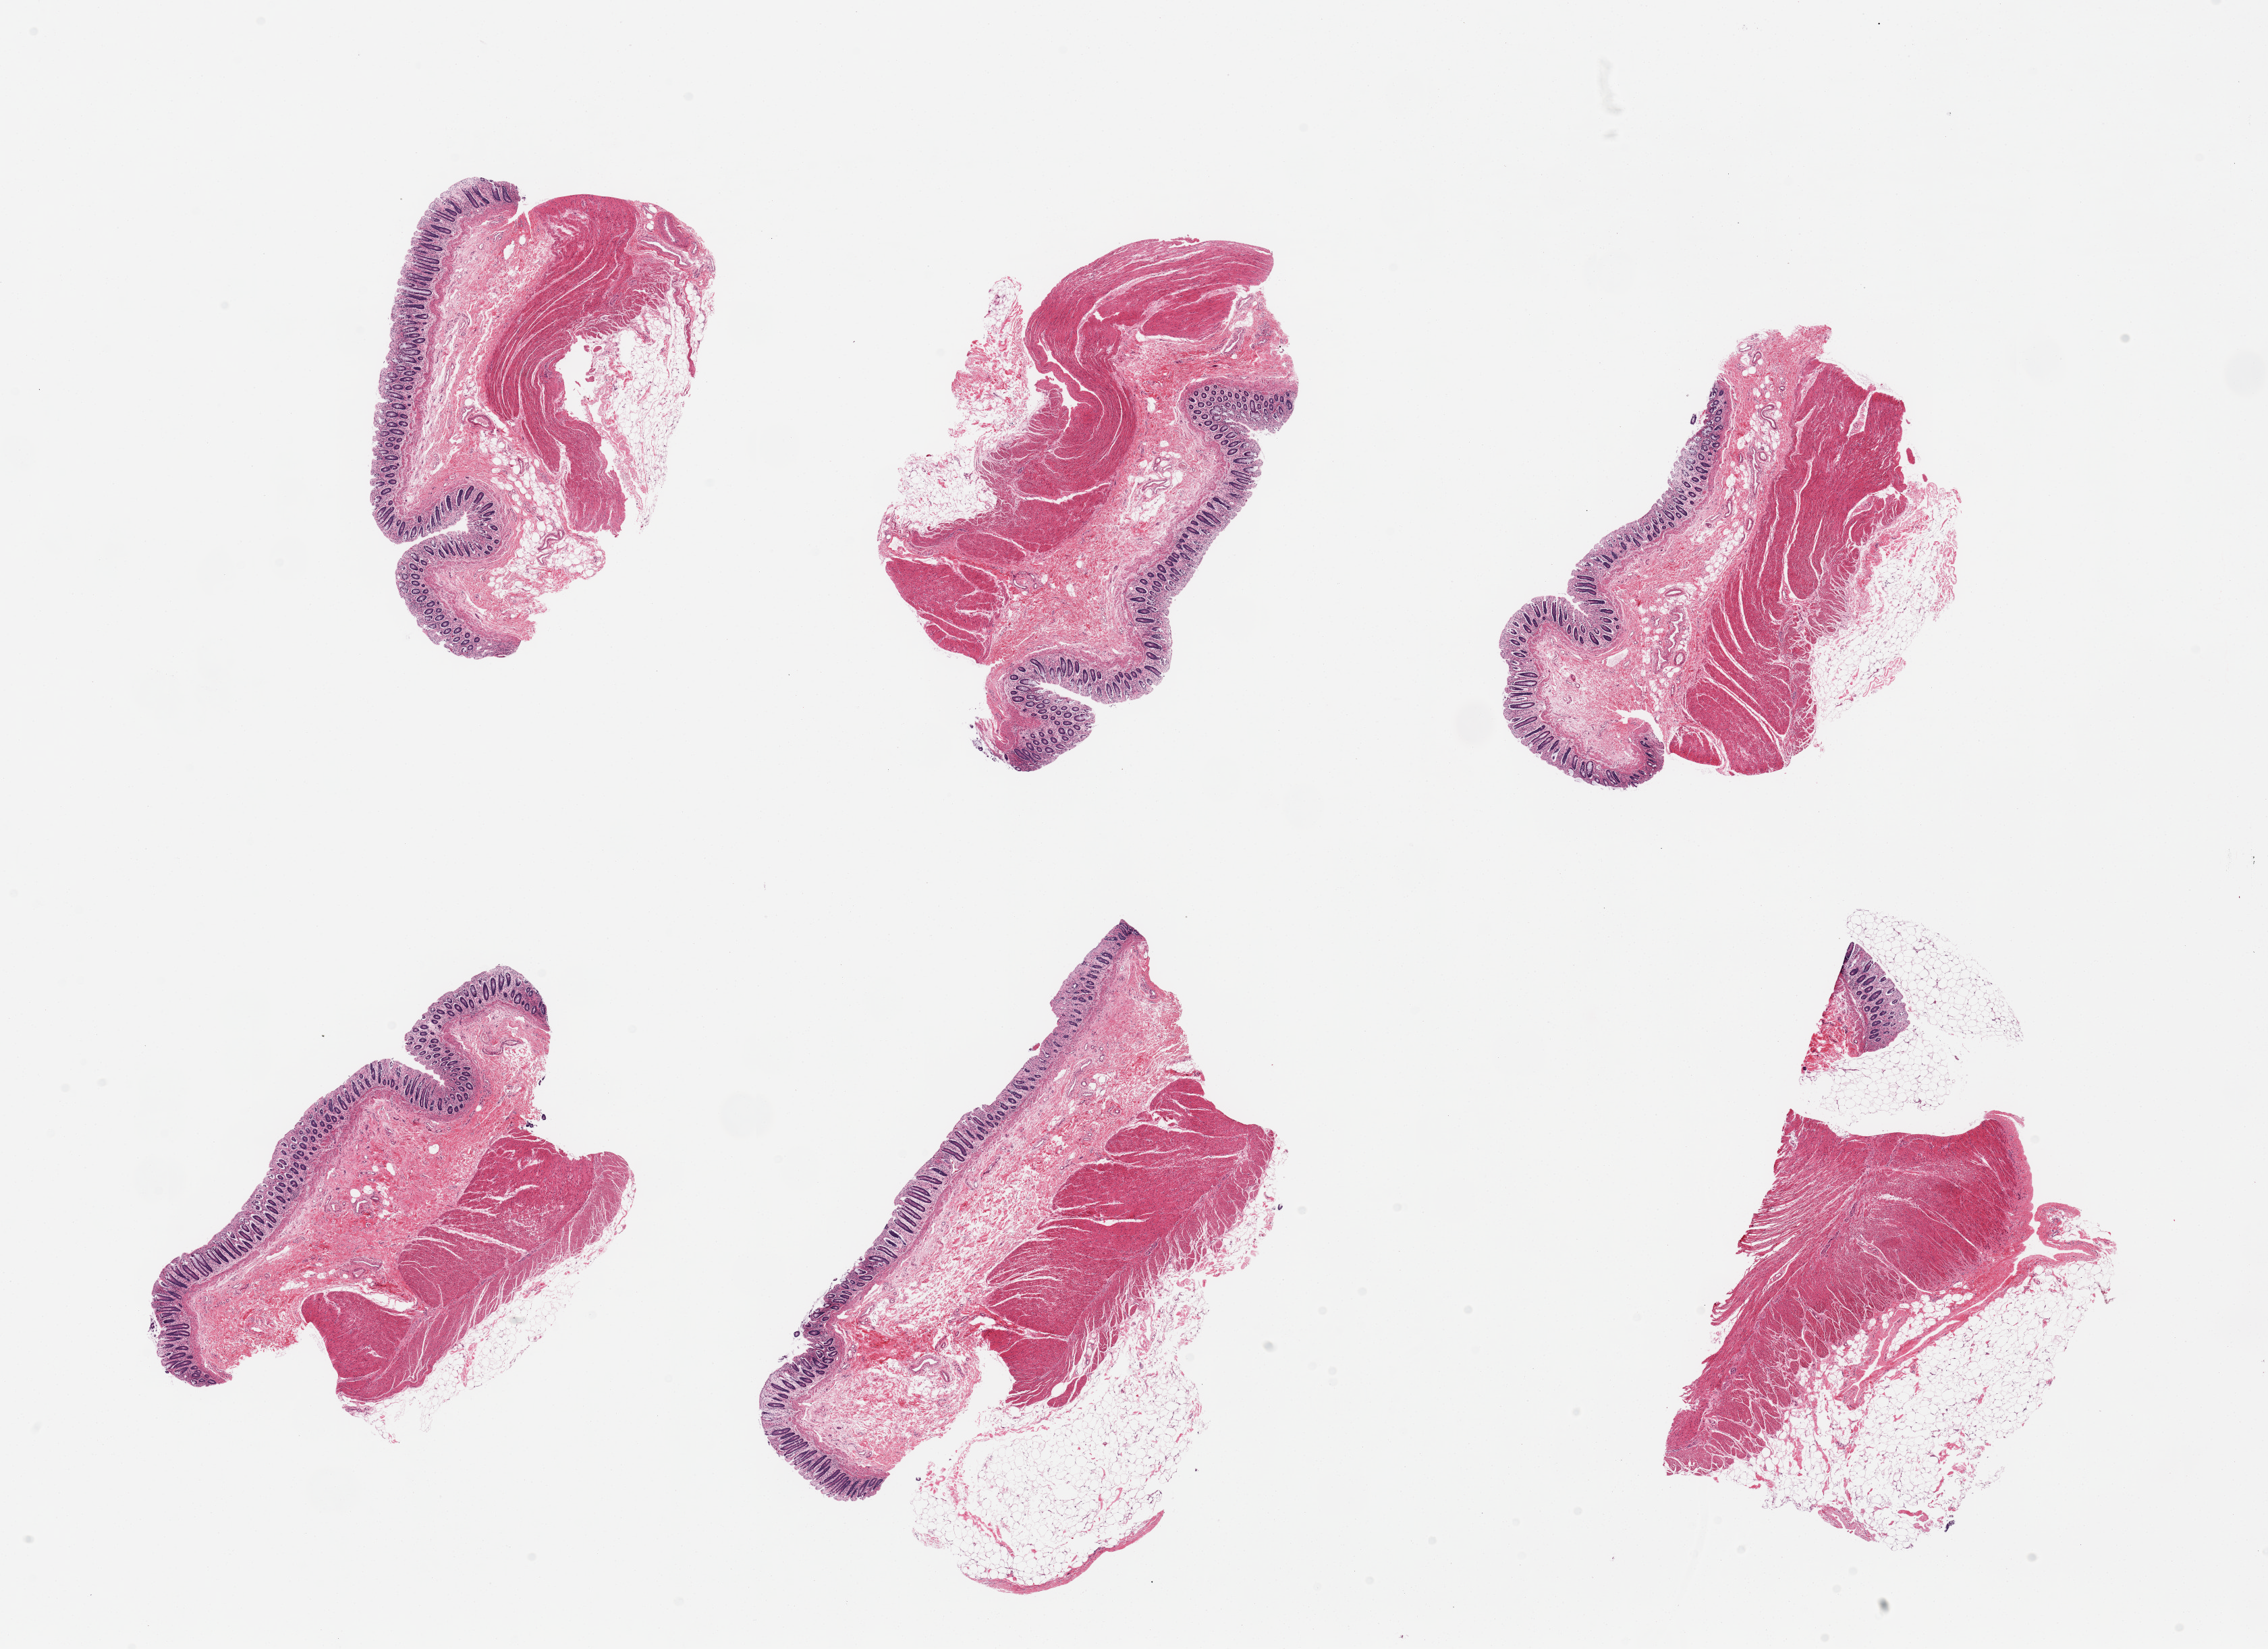
Haematoxylin and eosin whole-slide image — shown as a low-resolution overview of the whole scanned area (about 26.6 x 19.3 mm, from a 20x scan). Female donor.
* specimen: PAXgene-fixed, paraffin-embedded tissue; target tissue: sigmoid colon; donor tissue sample